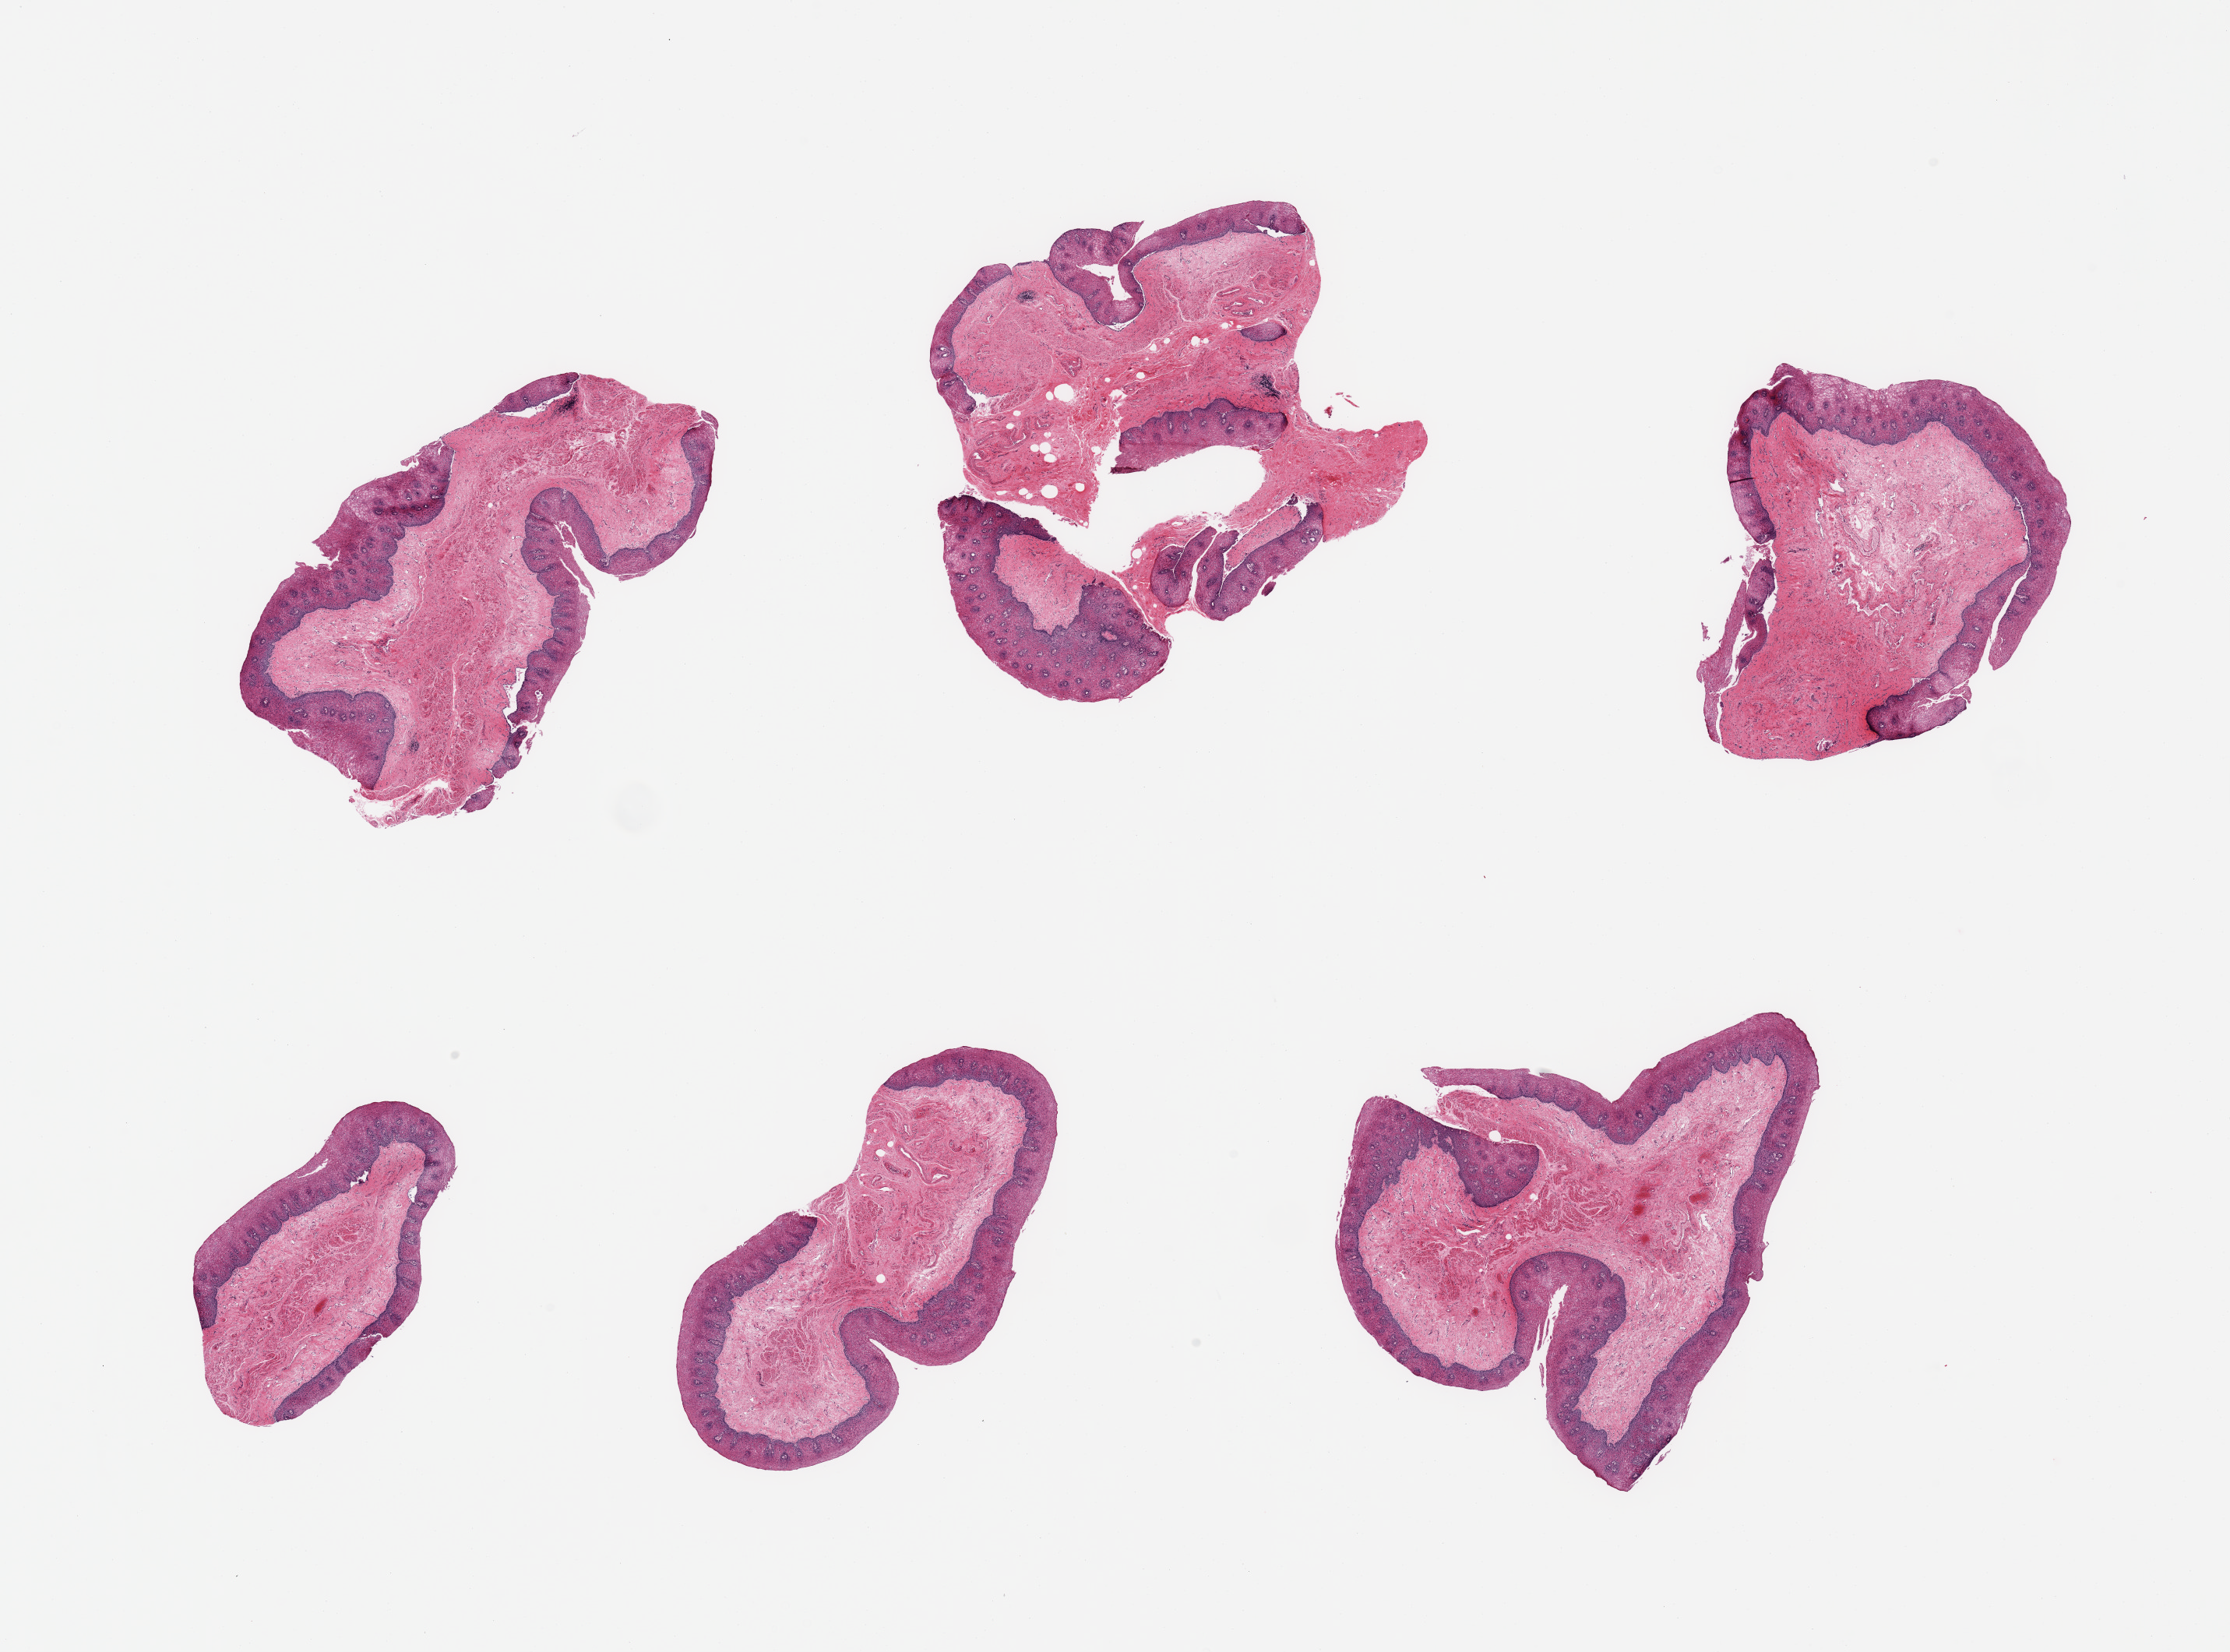
Whole-slide image, haematoxylin and eosin stain, brightfield — shown as a low-resolution overview of the whole scanned area (about 22.6 x 16.8 mm). PAXgene-fixed paraffin-embedded (PFPE) section. Section of esophageal mucous membrane (target tissue). Donor tissue sample. Donor: male.
Review note (as recorded): 6 pieces; target squamous mucosa up to ~0.5mm, ~15-20% of thickness.